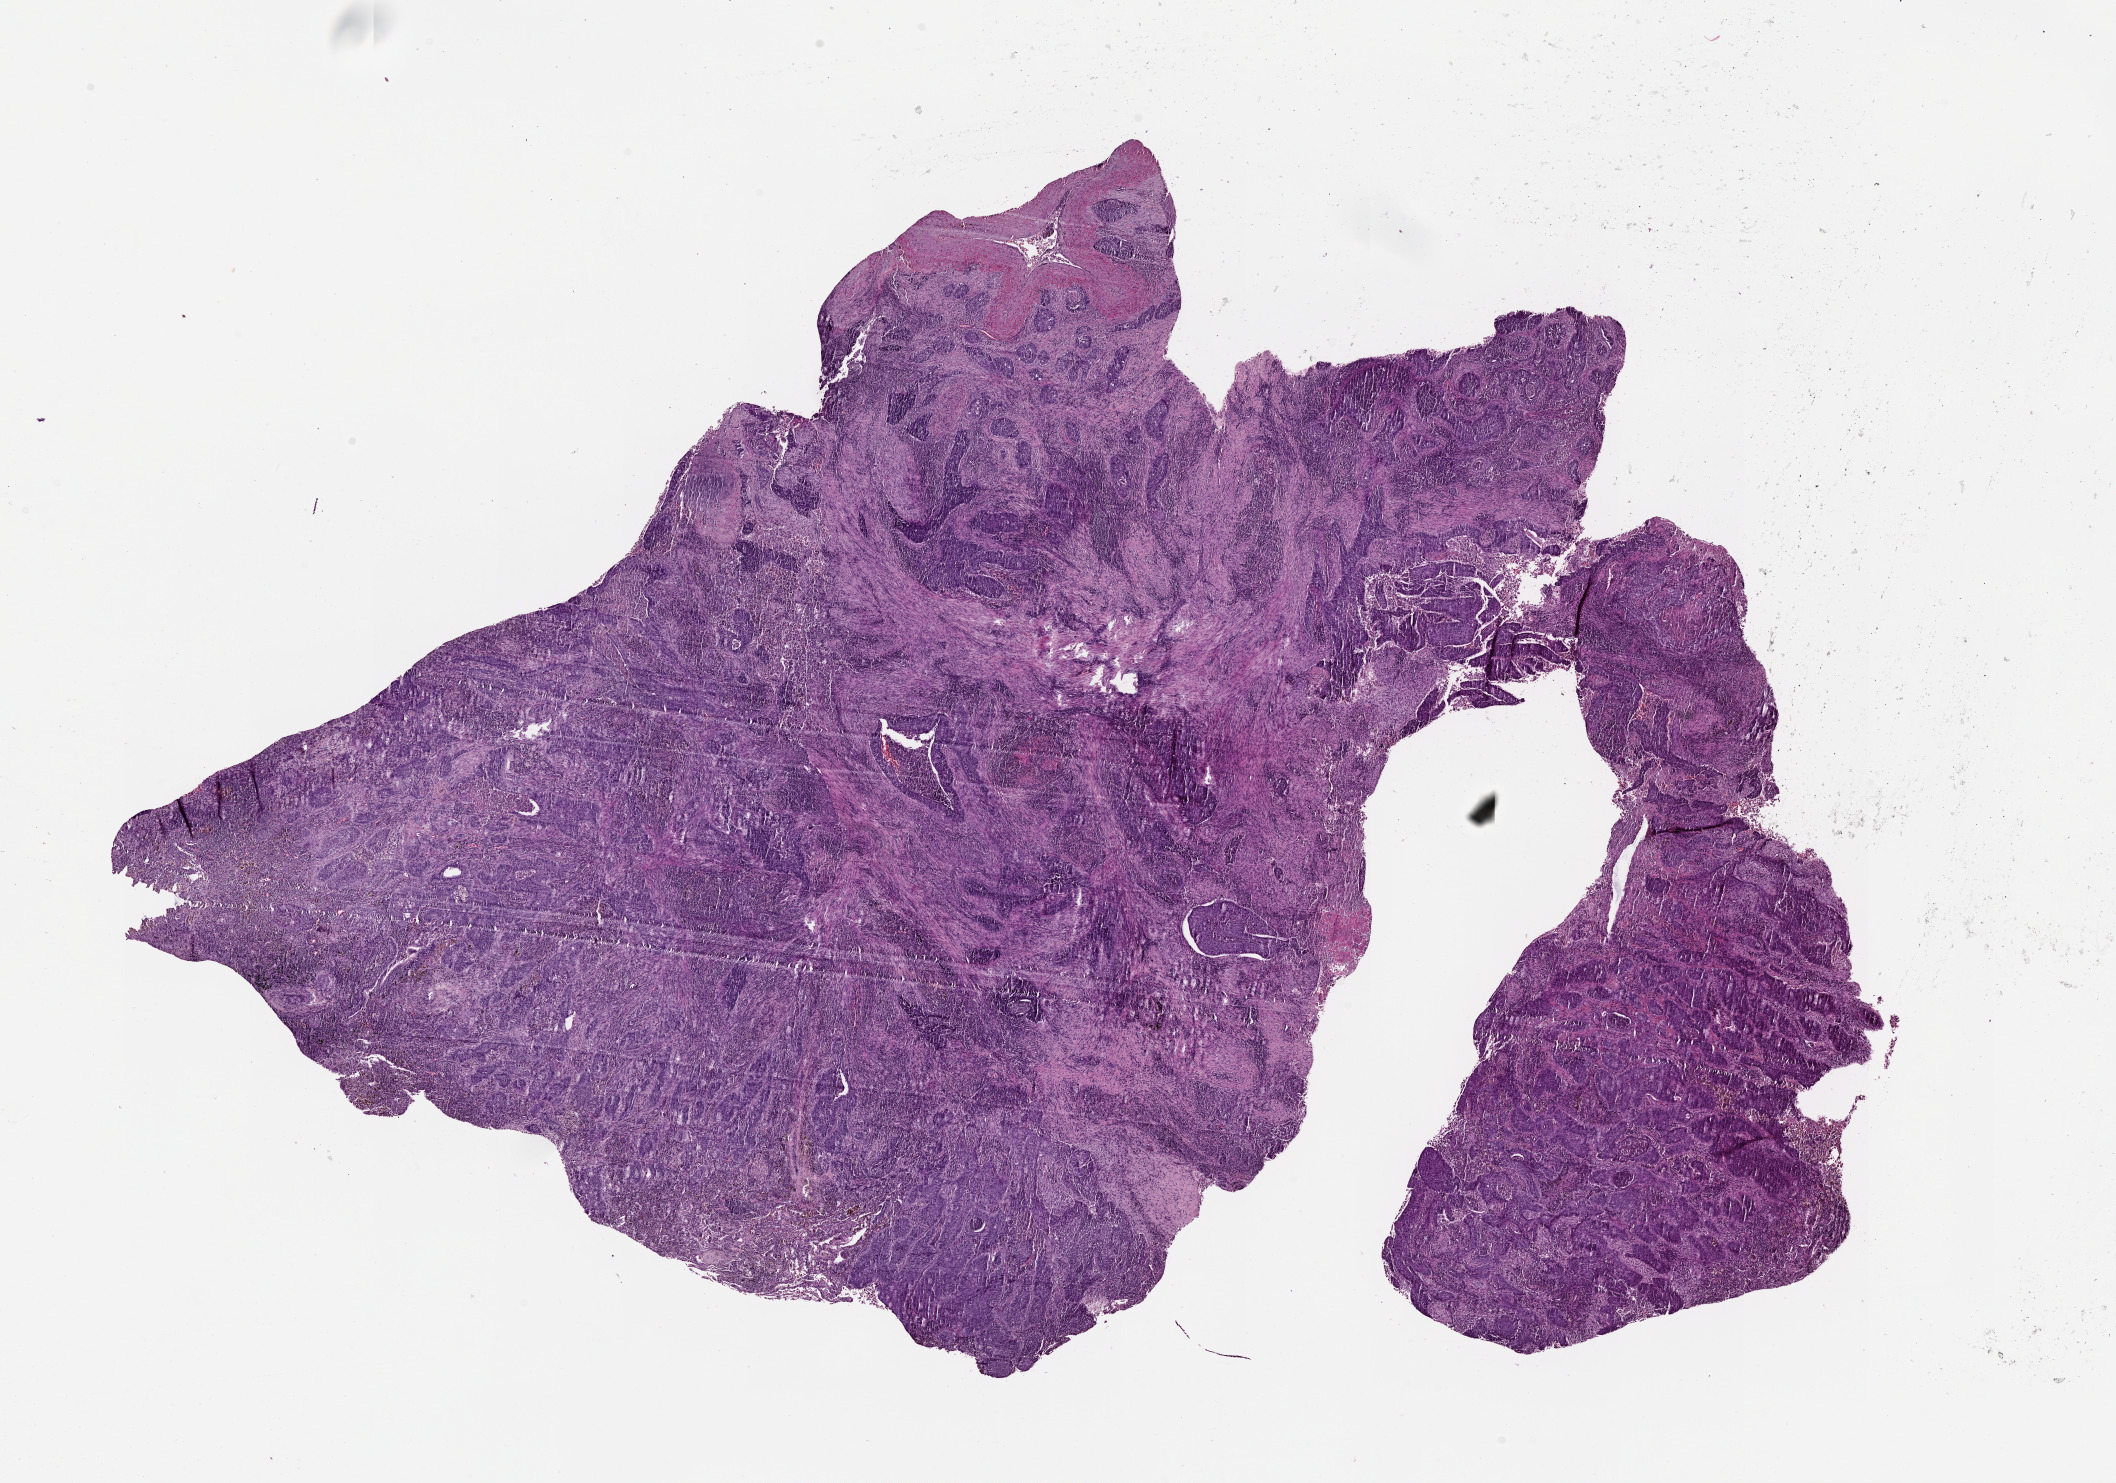
Whole-slide histology image, H&E-stained — a low-resolution overview of the entire scanned area, about 17.0 x 11.9 mm (acquisition: 20x scan). Tumour tissue sample, lung. Patient: male, age 59 years.
Patient diagnosis (cohort enrolment): squamous cell carcinoma (lung).